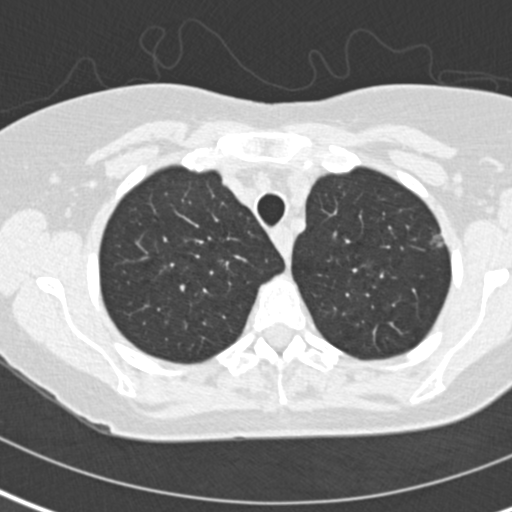
Low-dose screening chest CT, one axial slice; slice 117 of 141 in the series (ordered by position); 120 kVp; lung window (W 1500 / L -600 HU); 2 mm slice thickness; 512 × 512 image matrix.
Annotated regions visible in this slice (expert manual segmentation):
- lesion 1 (tumor, upper lobe of left lung): bounding box <433,233,444,247> (left, top, right, bottom; pixels)